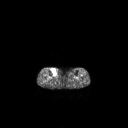
FDG PET of an extremity soft-tissue mass (from a PET/CT study), one axial slice. Position 140 of 267 along the scan axis. 128 × 128 image matrix. Female patient, age 65 years. From the clinical record (not read from this slice): histological type: undifferentiated – high grade; grade: high; site of the primary tumour: right thigh.
Outlined on this slice (expert contour drawn on MRI and transferred to this co-registered scan by the dataset authors):
- gross tumour volume (mass): box from (x=51, y=68) to (x=56, y=75) px